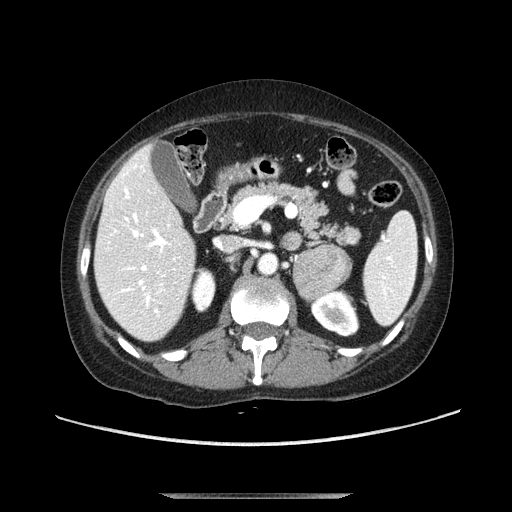
Contrast-enhanced abdominal CT, one axial slice. Slice 59 of 107 in the series (ordered by position). Soft-tissue window (W 400 / L 40 HU). 2.5 mm slice thickness. 512 × 512 image matrix, field of view 380 × 380 mm. Female patient. From the clinical record (not read from this slice): diagnosis: adrenocortical carcinoma; tumour side: left adrenal; tumour size at pathology: 7.5 cm; Ki-67 index: 9 %; stage (as recorded): 3.
Annotated regions visible in this slice (semi-automatically segmented with operator editing):
- mass: bounding box <293,243,352,300> (left, top, right, bottom; pixels)